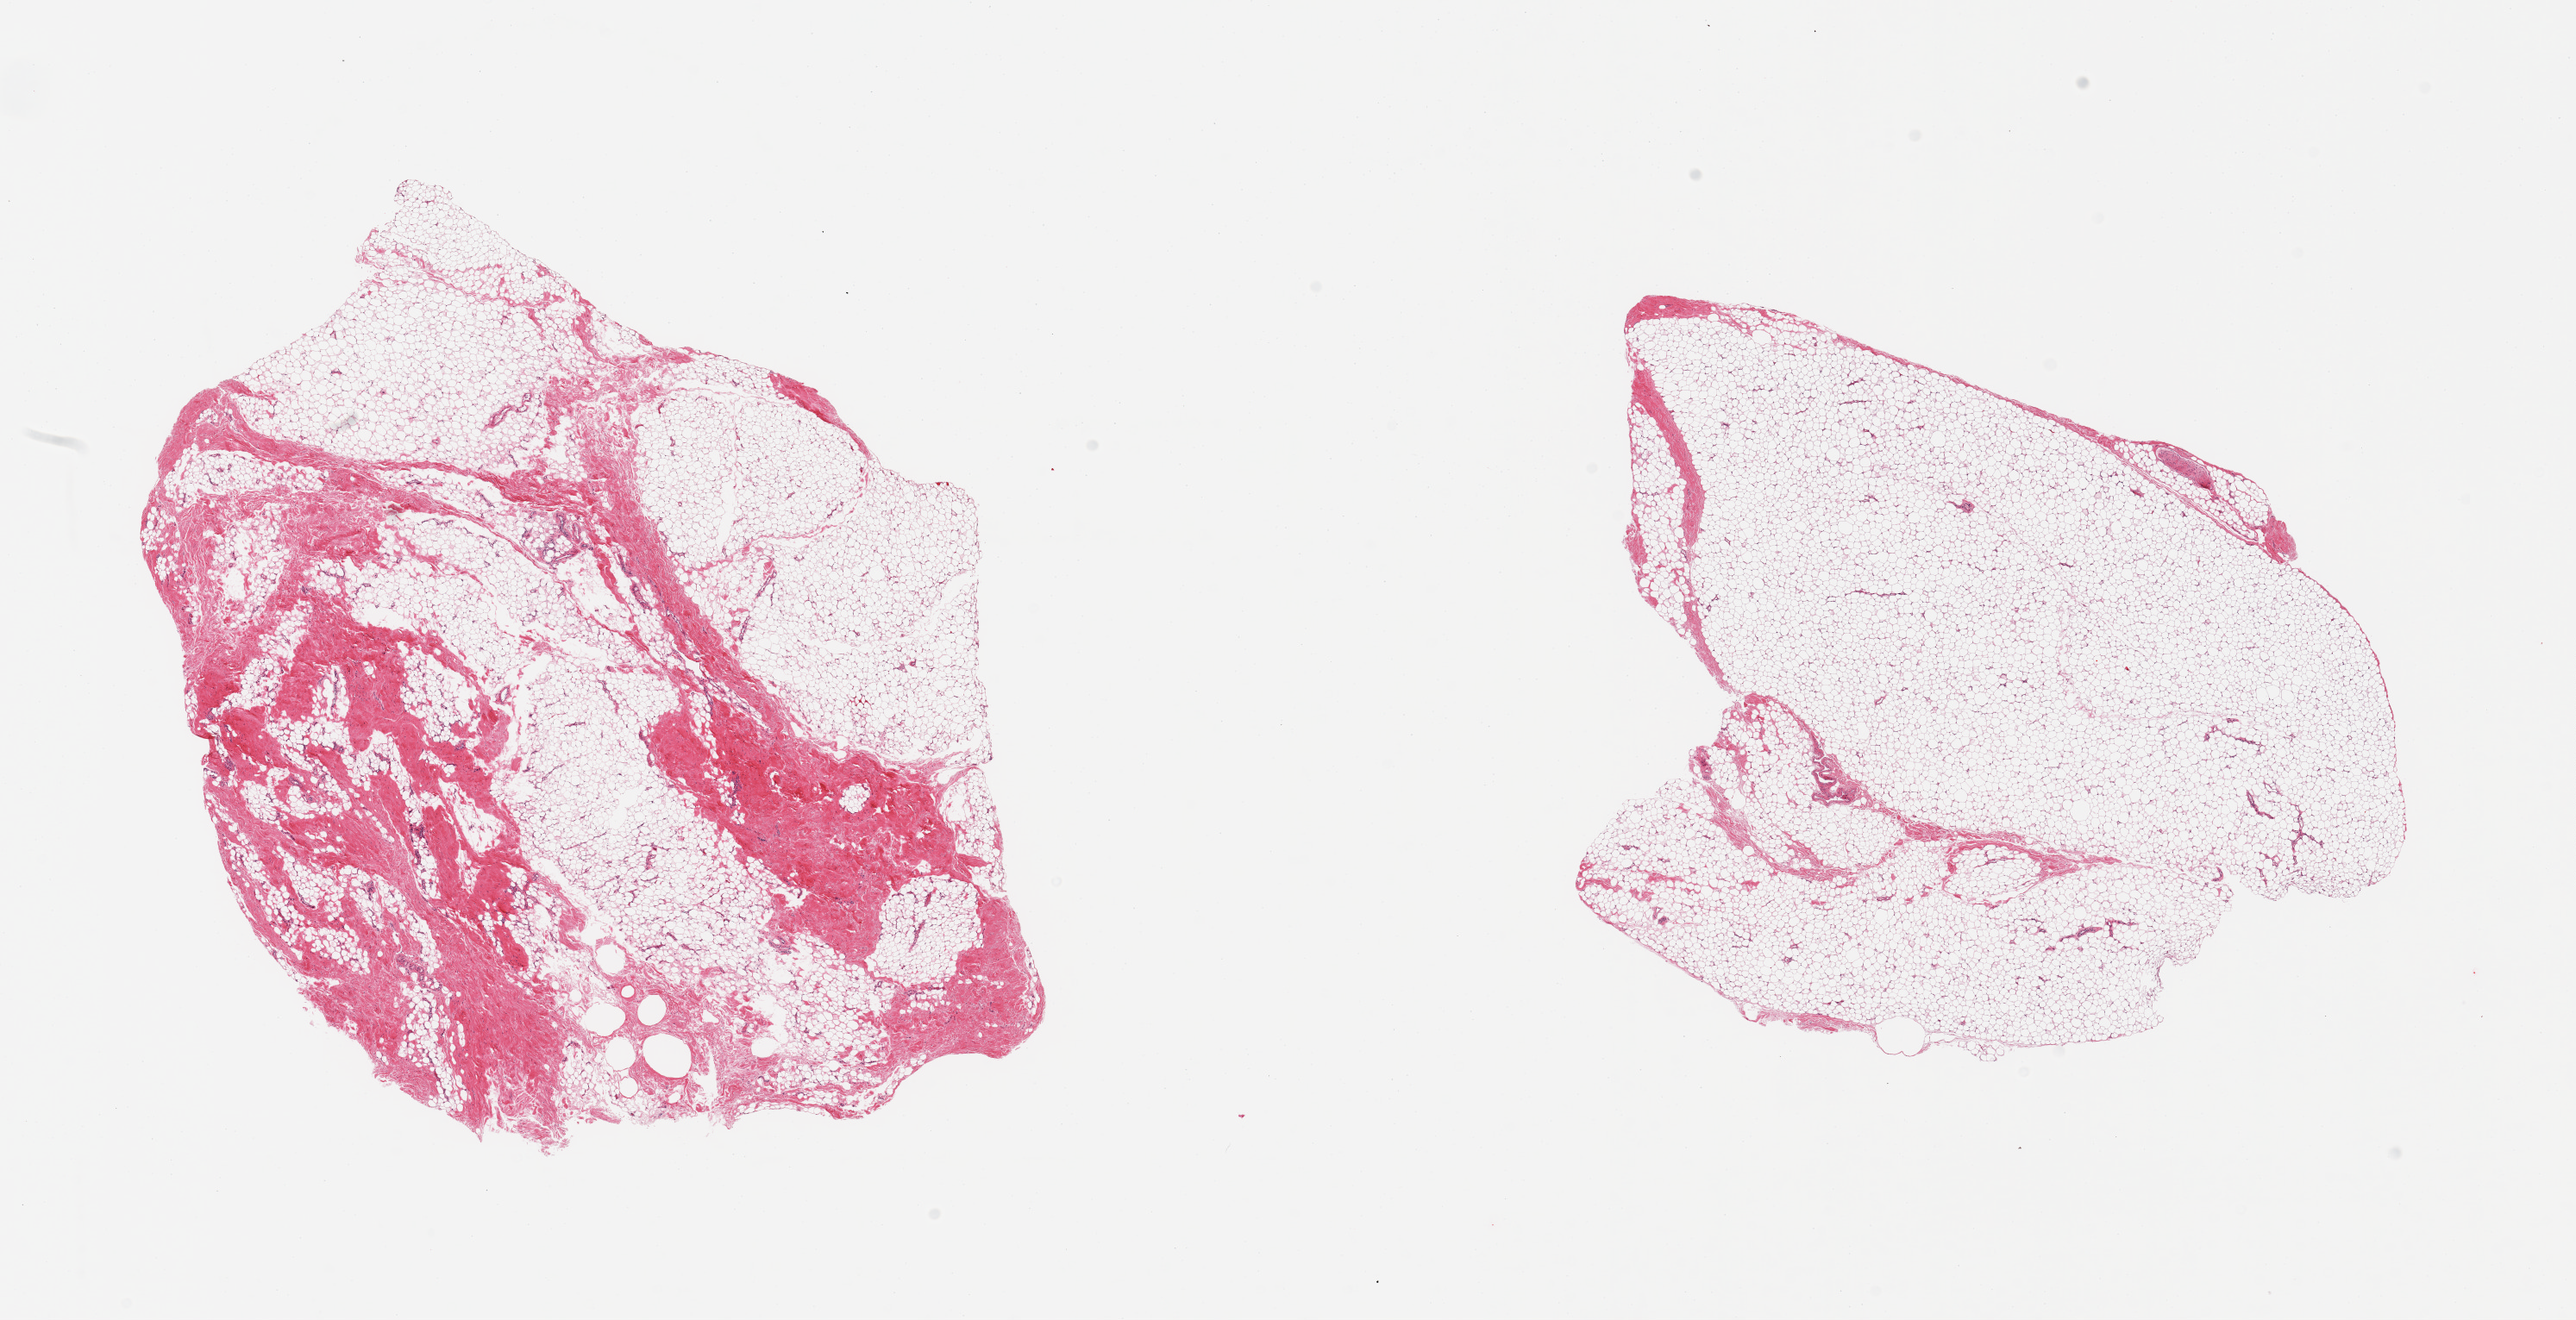
H&E whole-slide image — a low-resolution overview of the entire scanned area, about 23.6 x 12.1 mm, PAXgene-fixed, paraffin-embedded tissue, section of breast (target tissue), donor tissue sample. Donor sex: male.
Review note (as recorded): 2 pieces, ifbroadipose elements, no ductal elements.